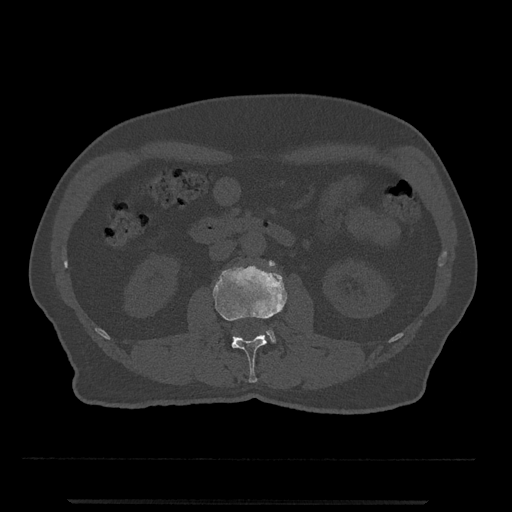
CT including the spine, one axial slice. Slice 251 of 797 in the series (ordered by position). Reconstruction kernel Br40s/3. Bone window (W 1800 / L 400 HU). 0.5 mm slice thickness. 512 × 512 image matrix, field of view 419 × 419 mm. Male patient, age 63 years. From the clinical record (not read from this slice): primary cancer: prostate.
Outlined on this slice (semi-automatic segmentation, software-assisted and operator-edited):
- L2 vertebra: box from (x=213, y=262) to (x=287, y=383) px
- L3 vertebra: (x=266, y=263)–(x=276, y=343)